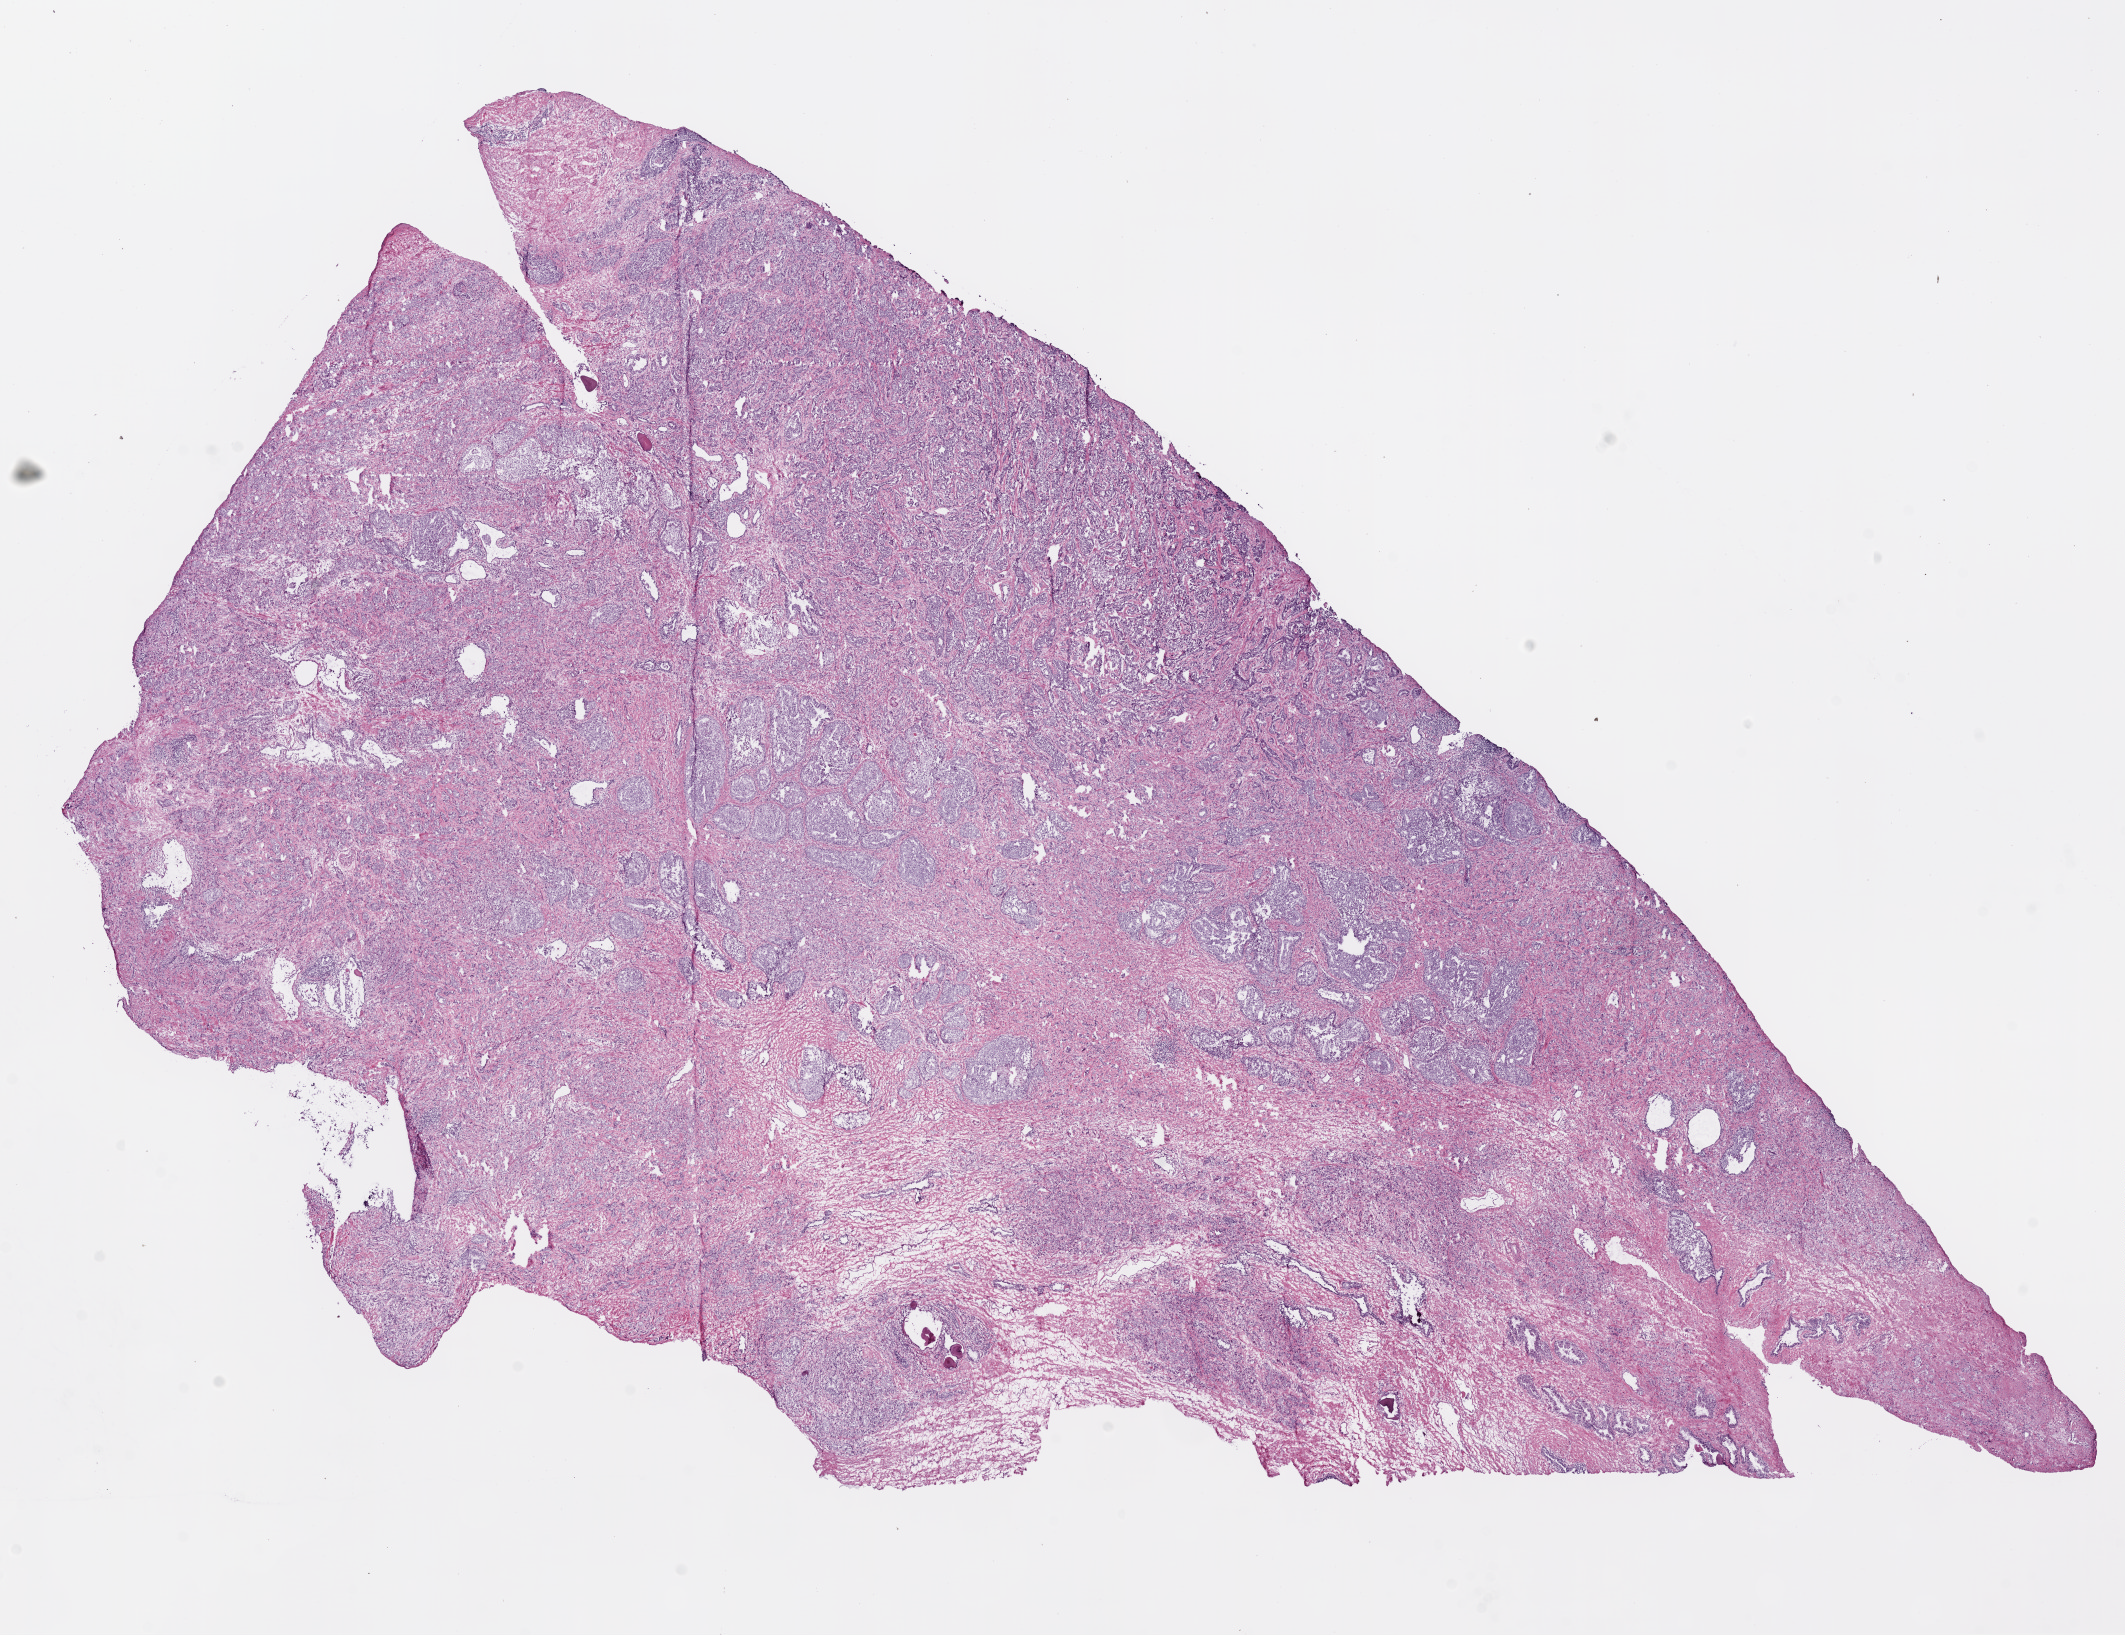
Whole-slide histology image, H&E-stained — a low-resolution overview of the entire scanned area, about 17.1 x 13.1 mm. Frozen section from the bottom of the tissue portion. Prostate, primary tumour sample. Patient: male, age at initial diagnosis 57 years. Gleason score: 9 (4+5). Pathologist review of this section (percent, as recorded): tumour cells 70%, tumour nuclei 75%, normal cells 10%, stromal cells 20%, necrosis 0%. Infiltration values recorded for this section: lymphocyte infiltration 2%, monocyte infiltration 0%, neutrophil infiltration 0%.
Laterality: bilateral. Diagnosis: Acinar cell carcinoma (prostate gland). Lymph nodes positive (case pathology): 0 of 17 examined.